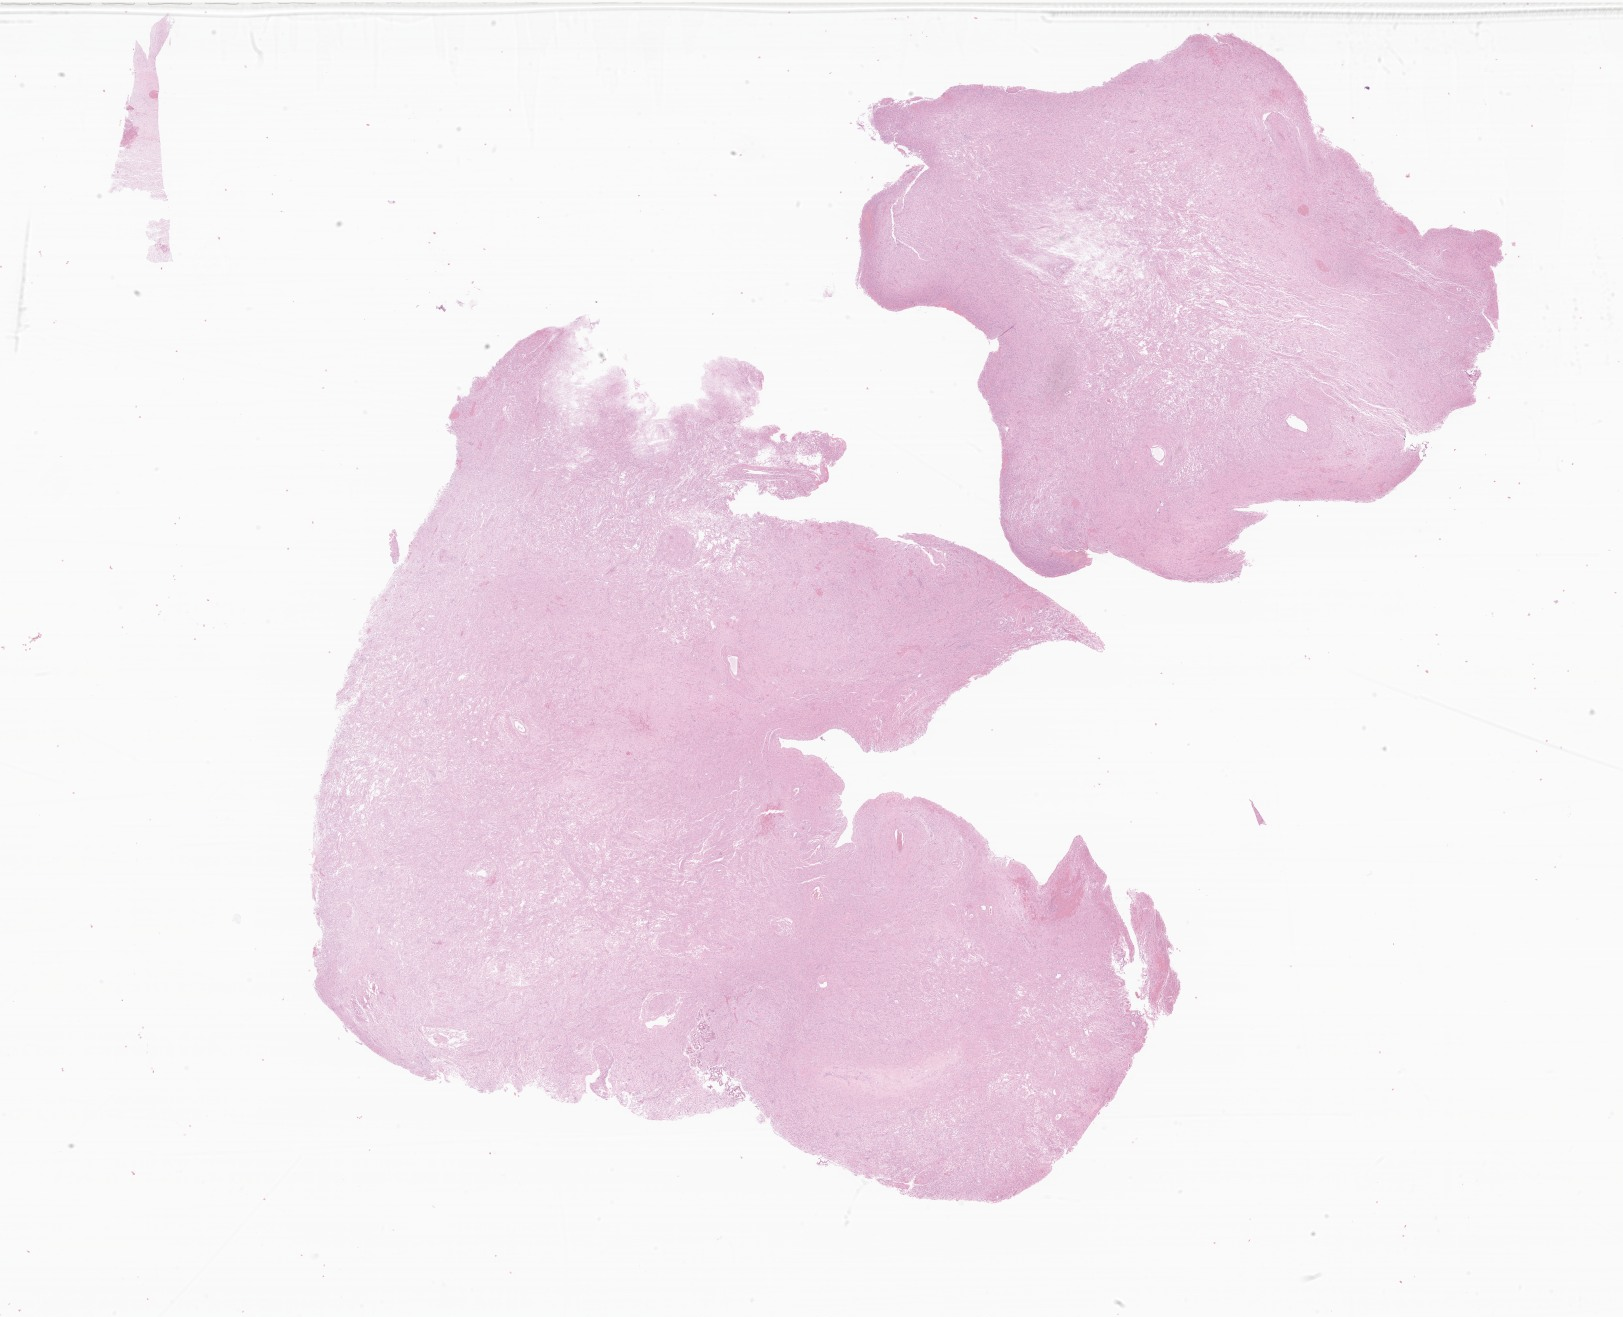
Whole-slide image, hematoxylin and eosin (H&E) stain of tumor tissue from the brain, low-resolution overview of the scanned area, about 27.4 x 22.2 mm. FFPE section. Patient male; age 89 months (7 years 5 months).
Recorded diagnosis: Pilocytic astrocytoma.